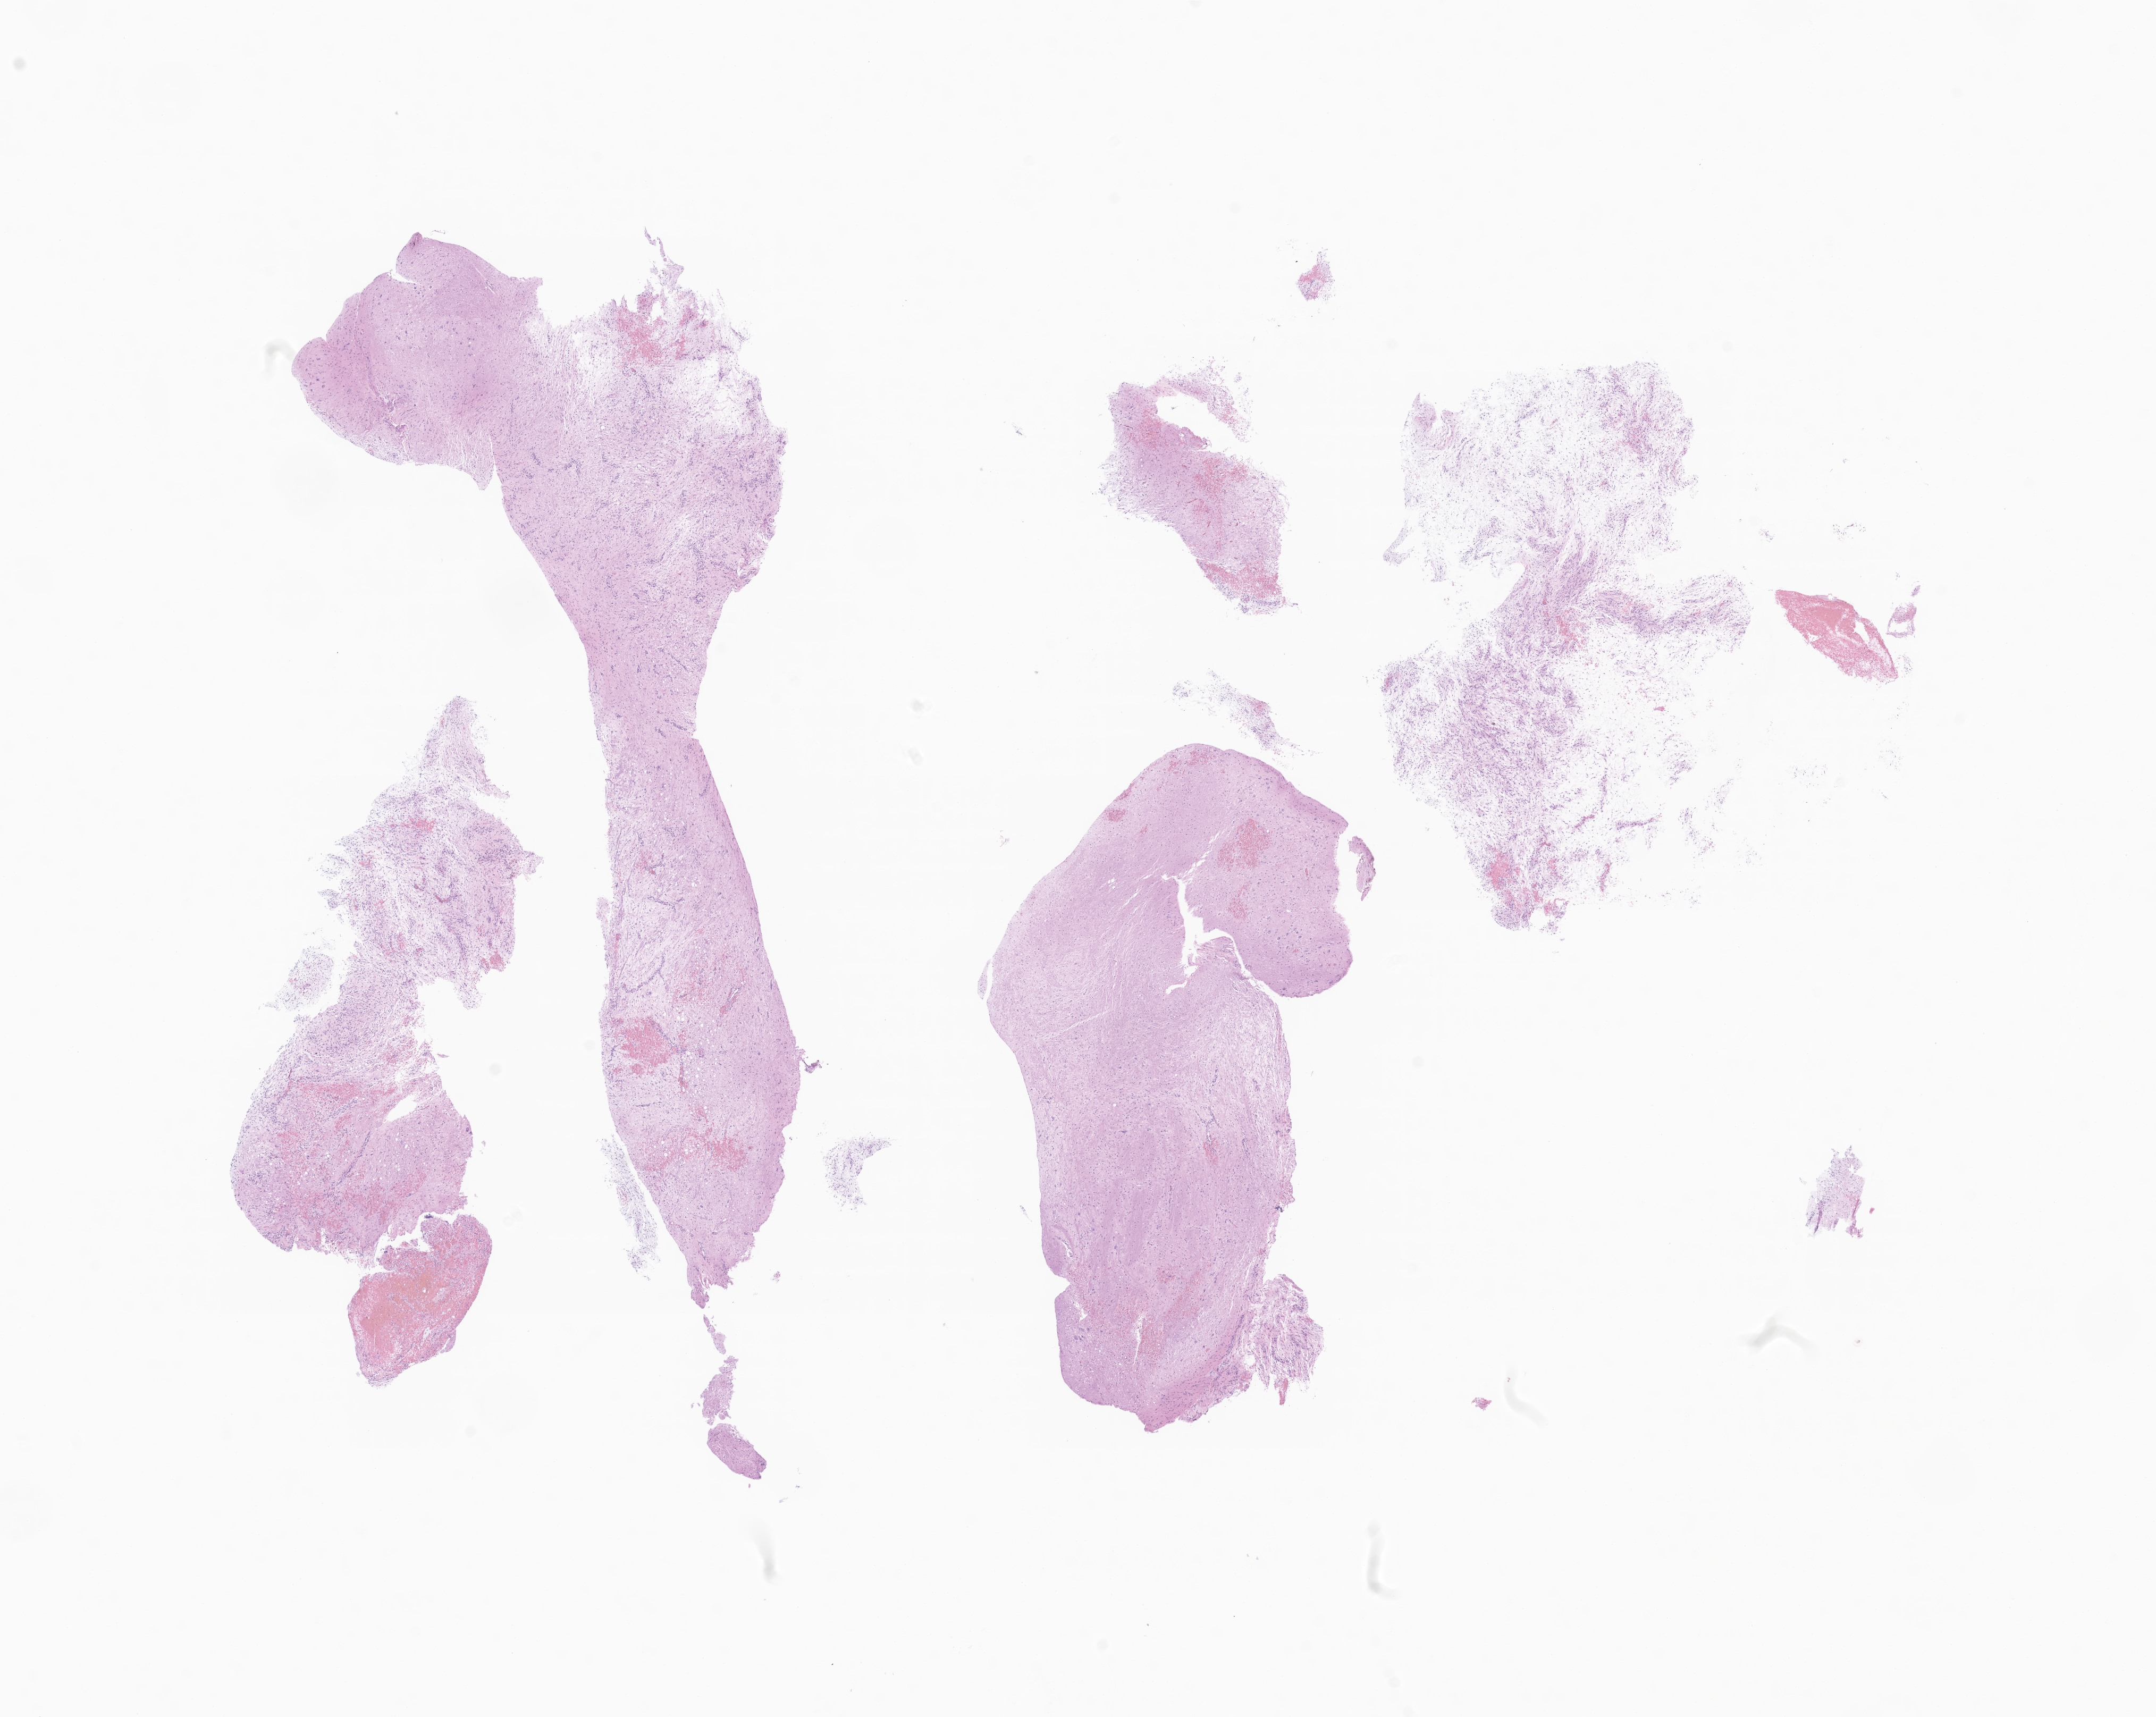
Whole-slide image, hematoxylin and eosin (H&E) stain of tumor tissue from the brain — whole scanned area (about 17.1 x 13.6 mm) shown as a low-resolution overview. Formalin-fixed paraffin-embedded section. Male patient, age 211 months (17 years 7 months).
Recorded diagnosis: Astrocytoma, NOS.